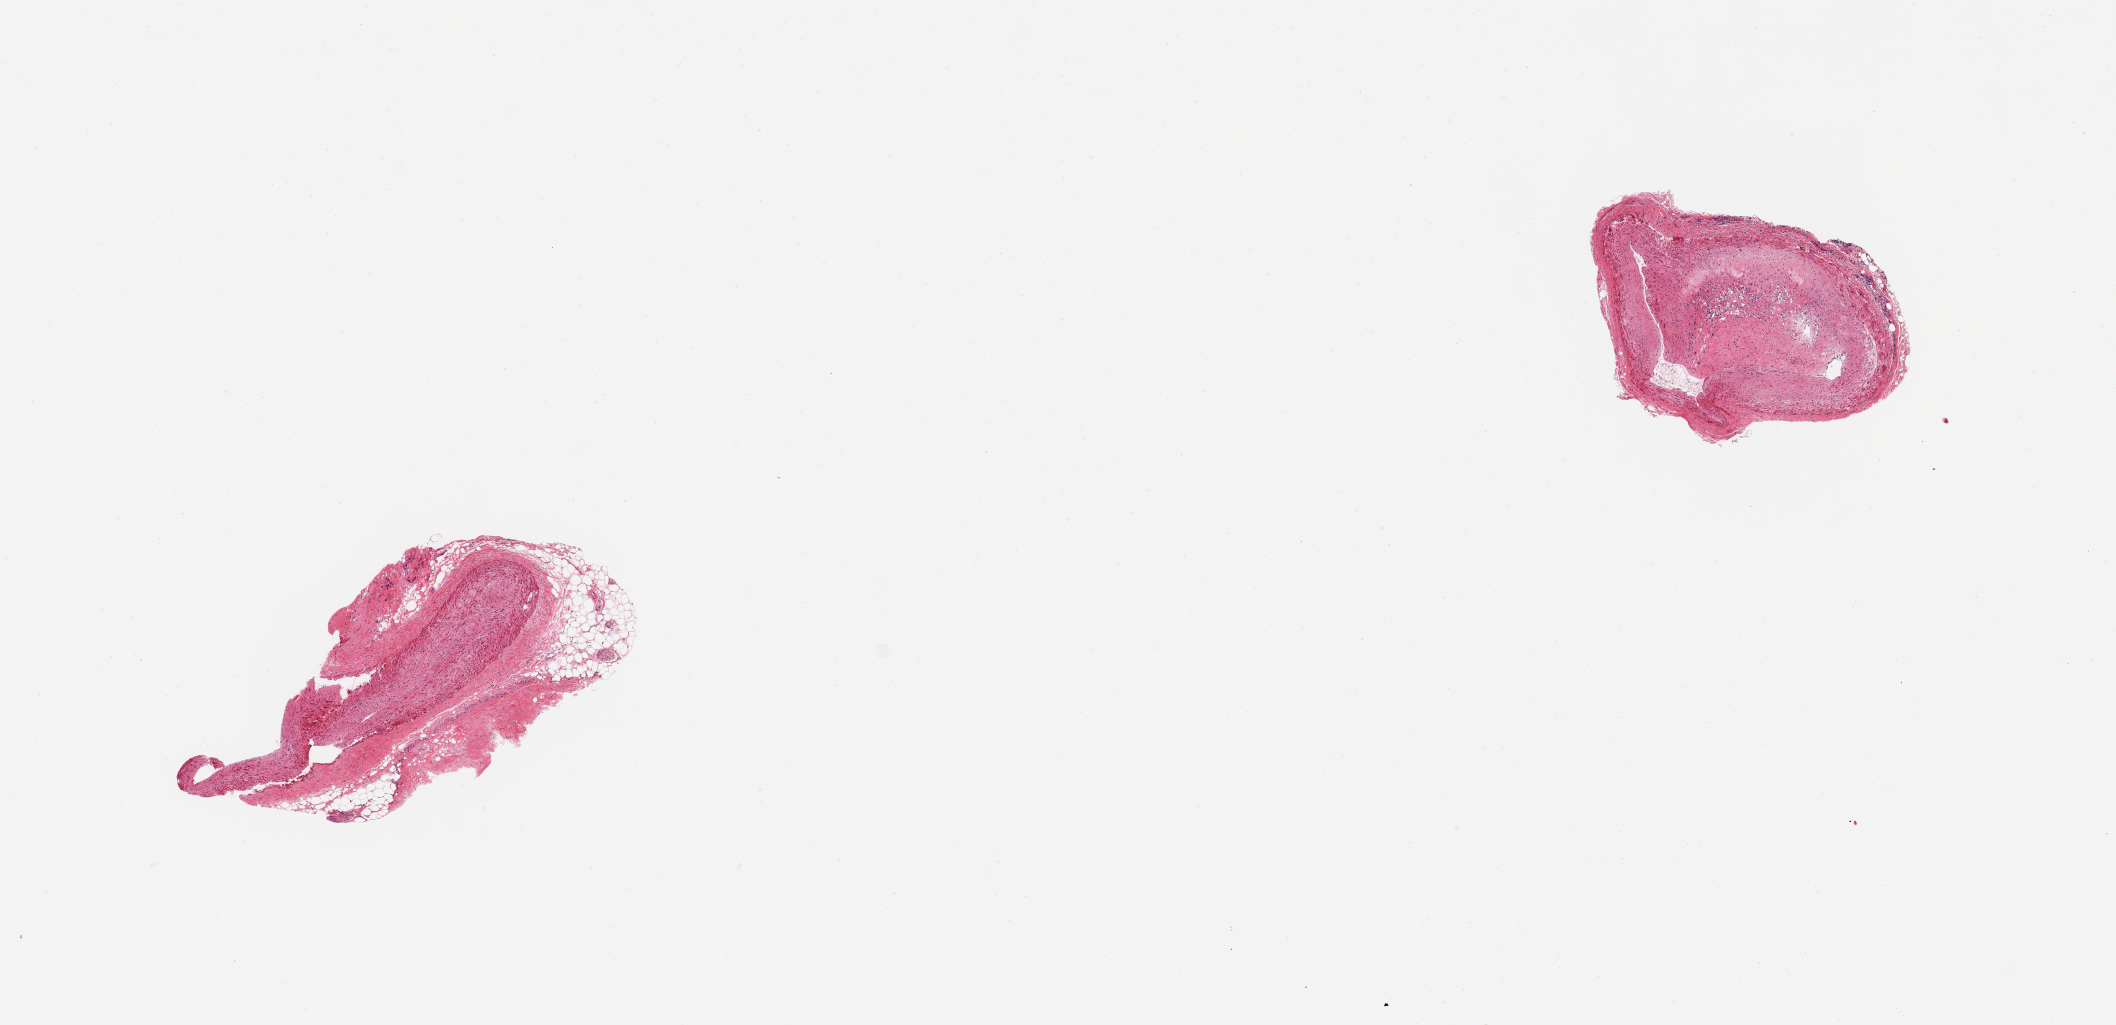
Digitized hematoxylin and eosin (H&E)-stained section, low-resolution overview of the scanned area, about 16.7 x 8.1 mm (acquisition: 20x scan). PAXgene-fixed, paraffin-embedded tissue. Sampled site (target tissue): coronary artery. Donor tissue sample.
* review note (as recorded): 2 pieces; prominent fibrofatty plaque; 30% external fat & fibrous stroma on 1 piece